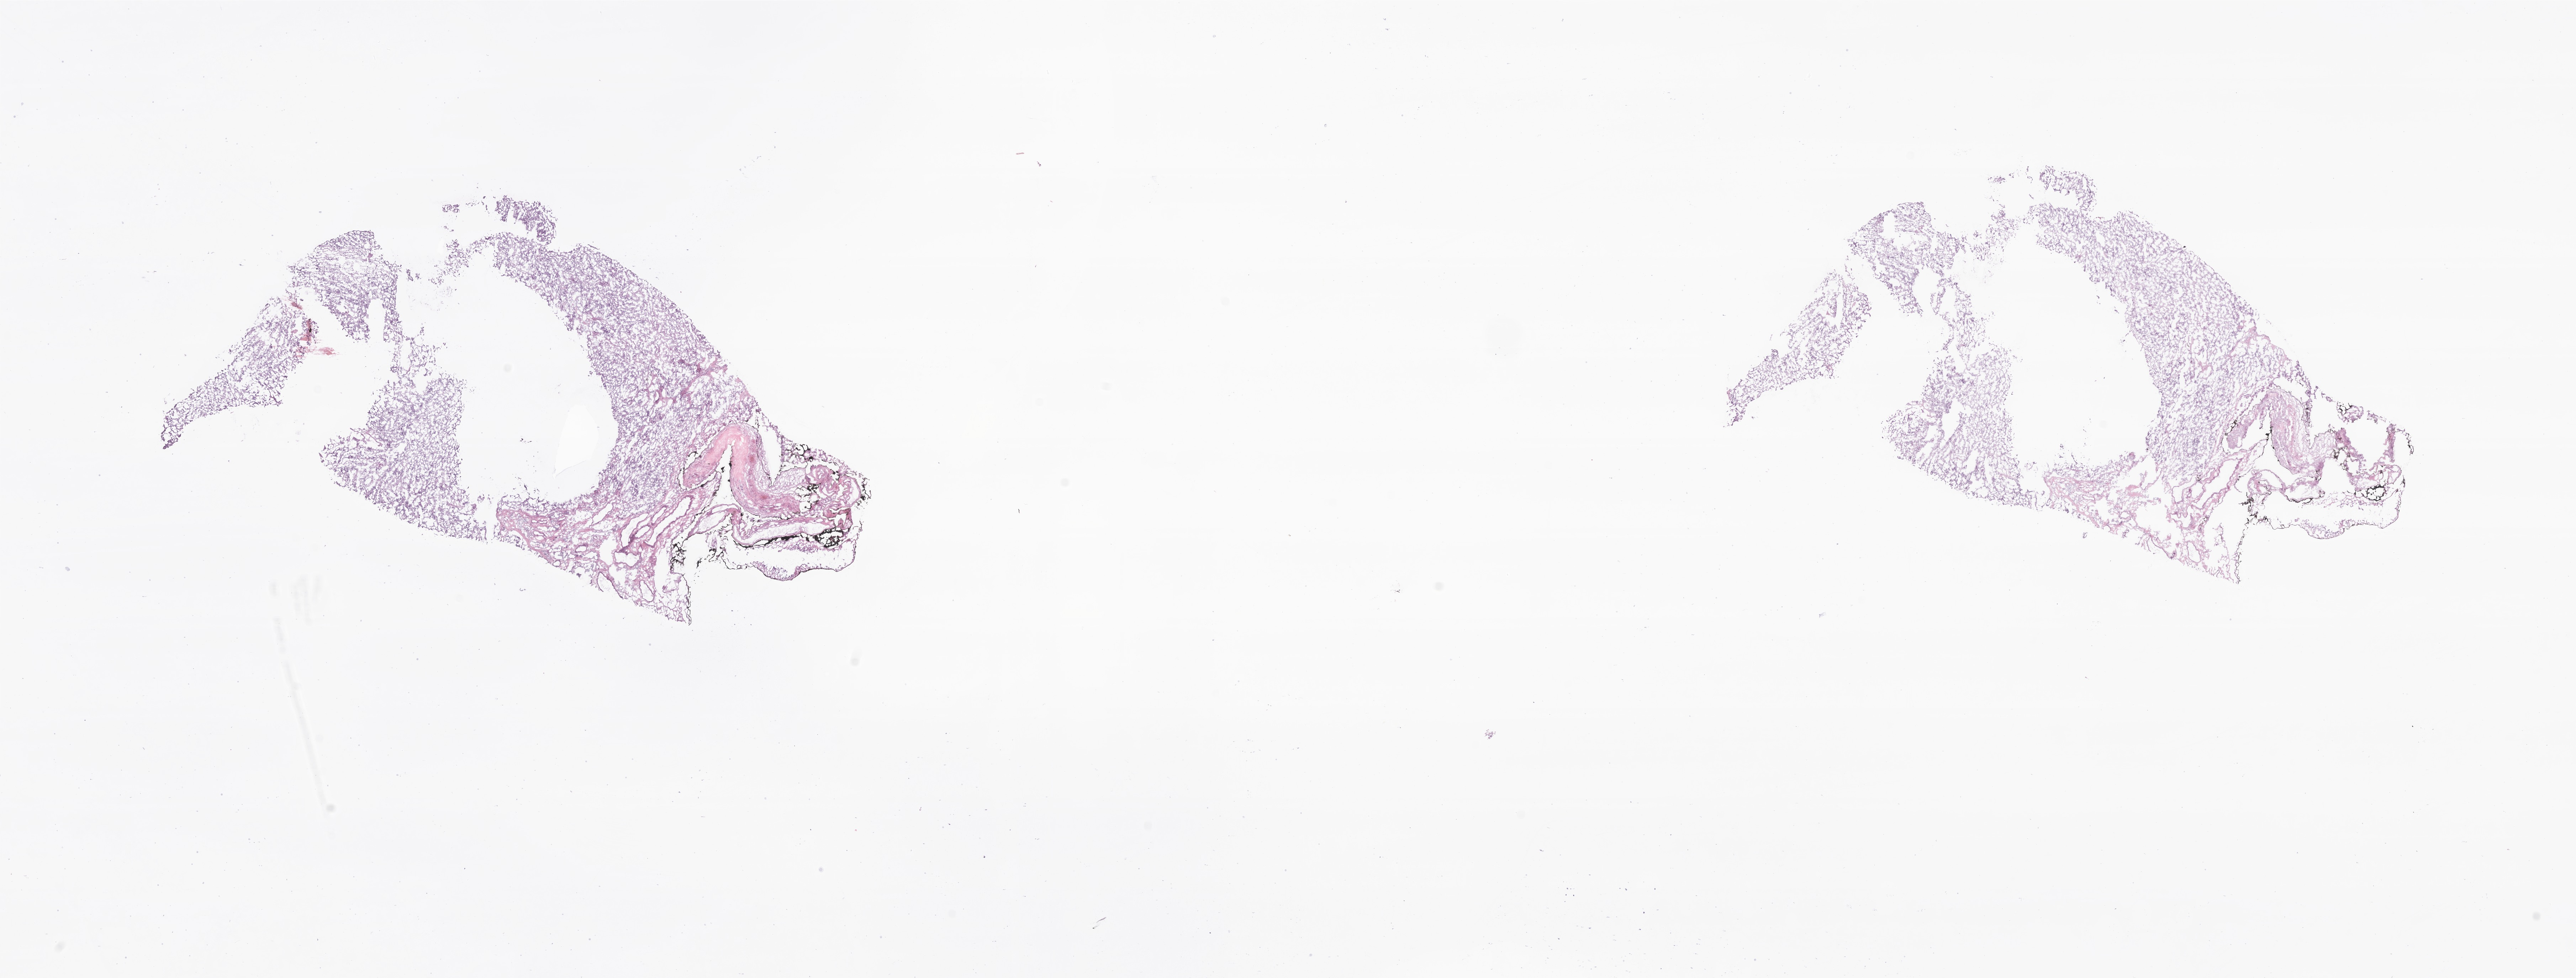
Digitized haematoxylin and eosin-stained section of tumor tissue from the spinal cord, low-resolution overview of the scanned area, about 30.5 x 11.6 mm, cryosection (OCT / tissue freezing medium). Female patient, age 156 months.
* diagnosis (ICD-O-3 morphology term): Ependymoma, NOS